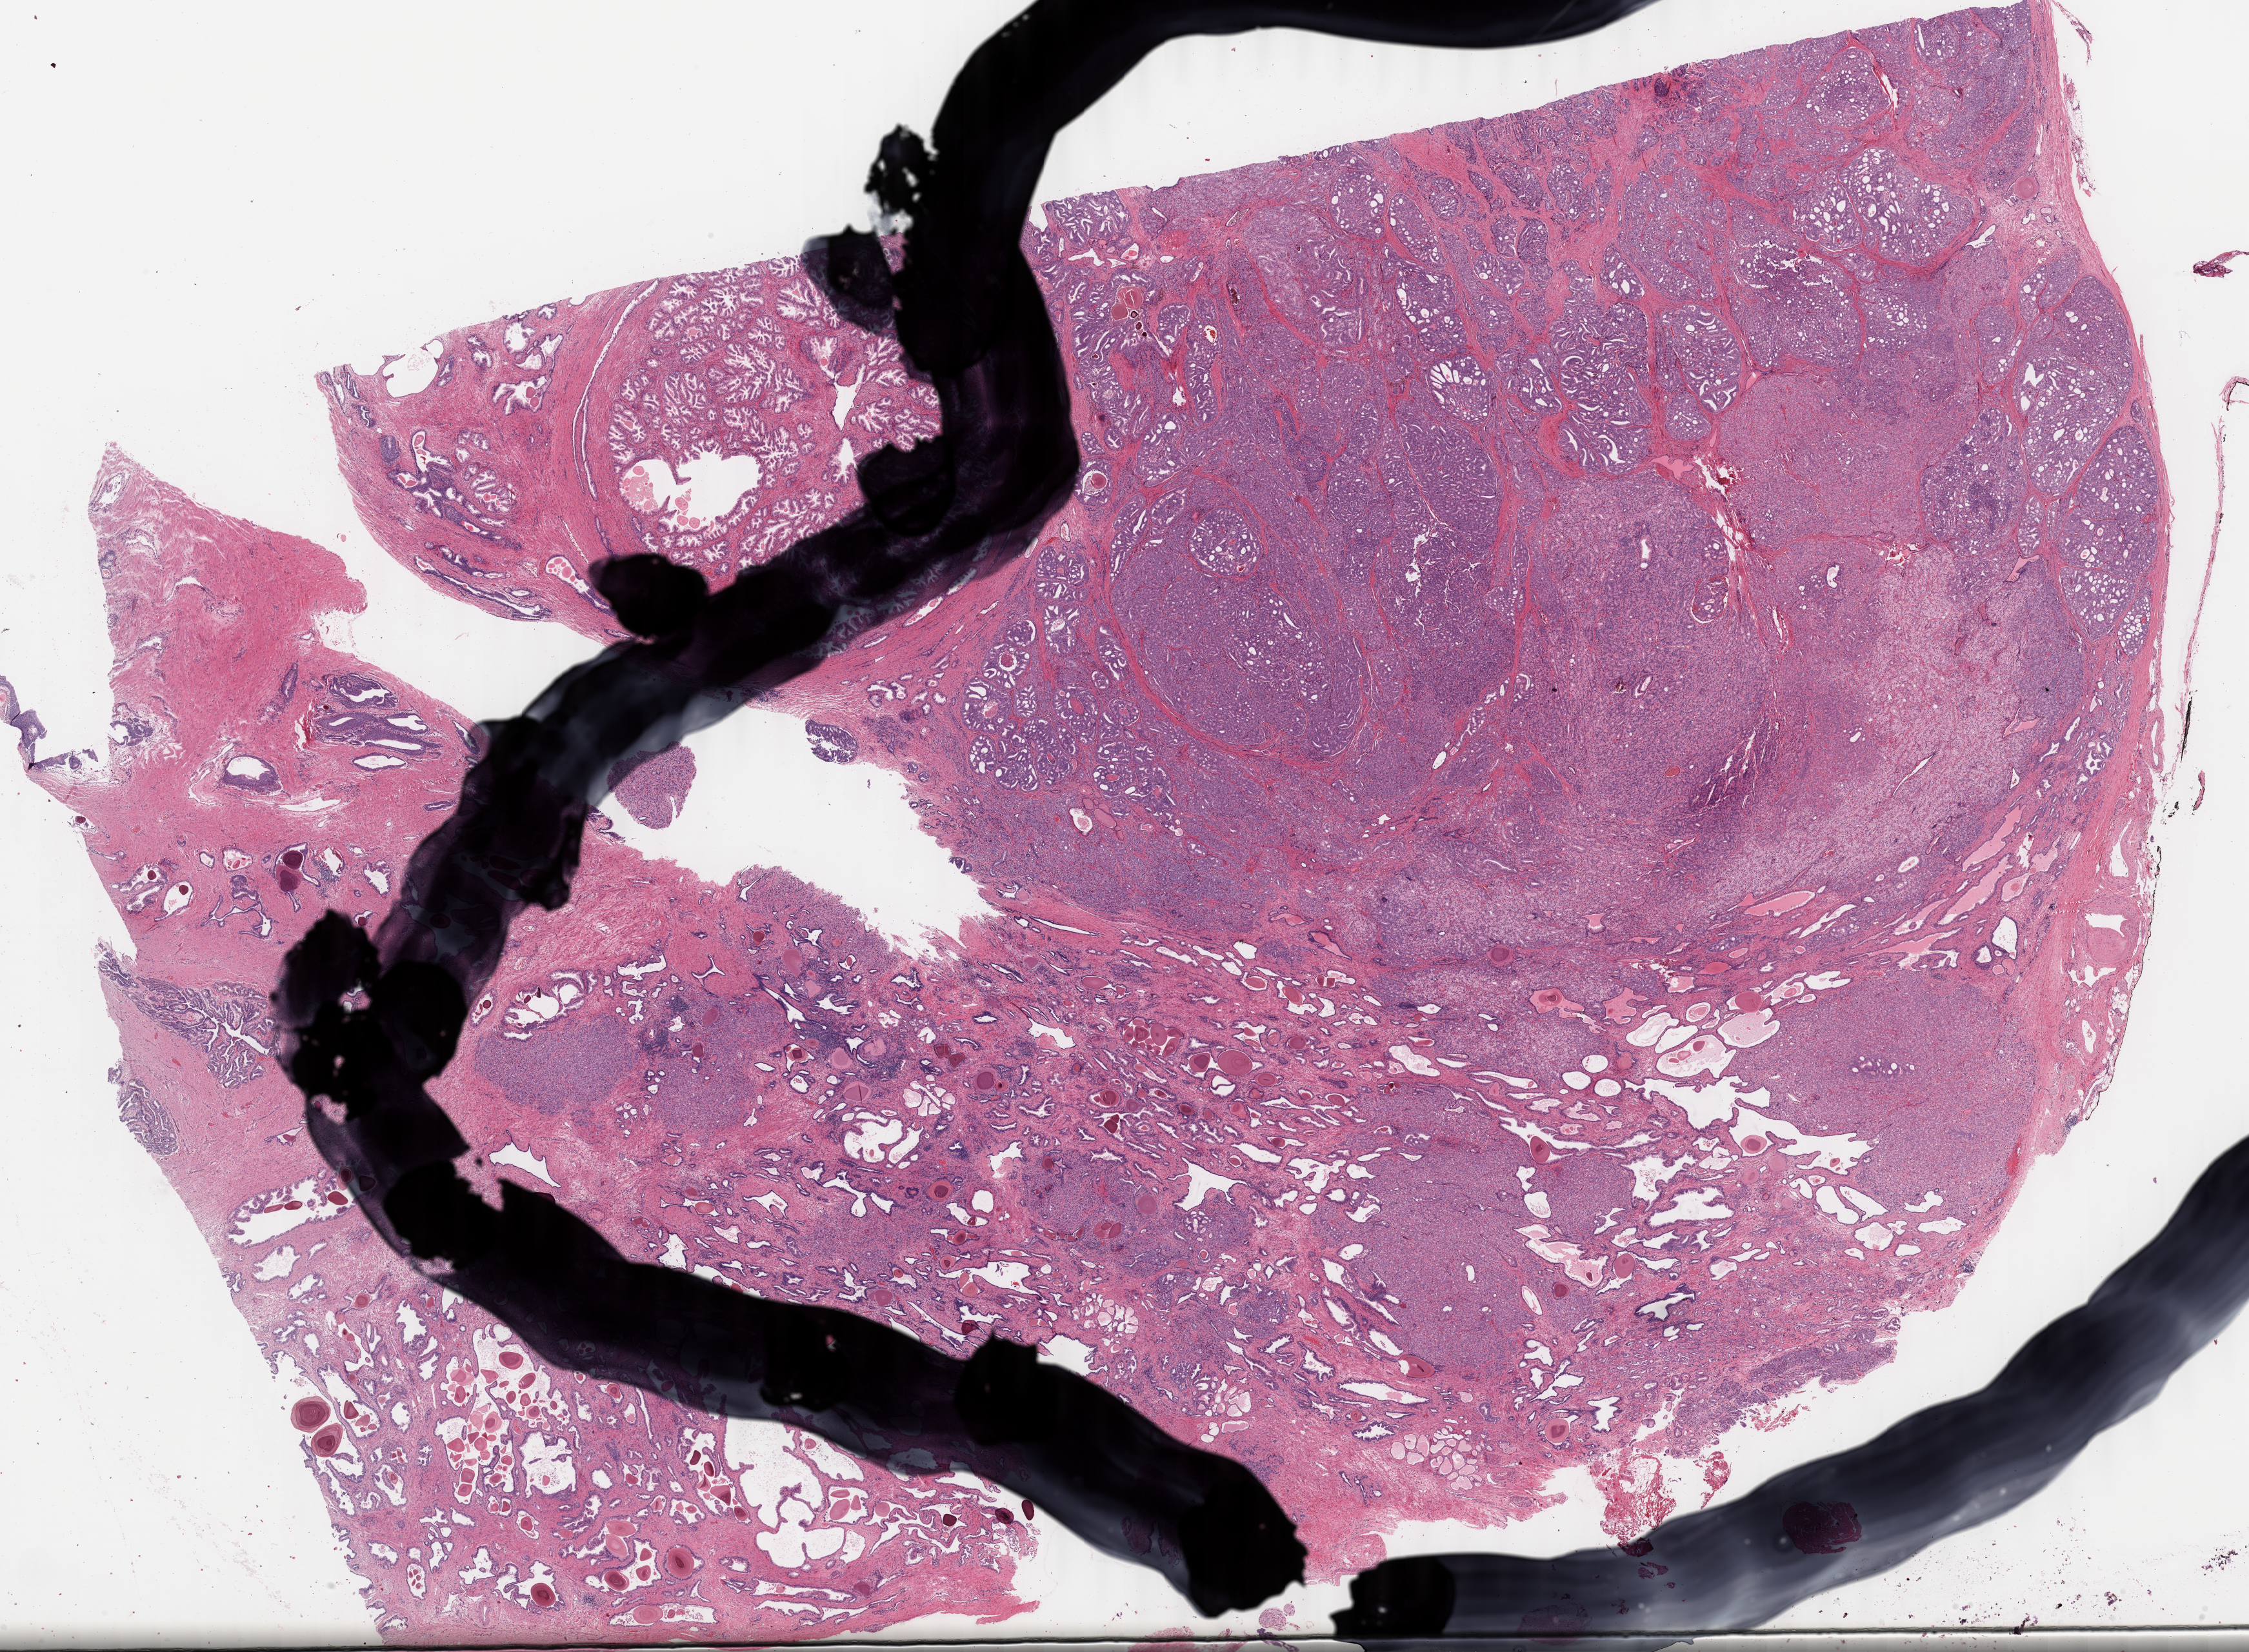
Whole-slide histology image, Hematoxylin and eosin (H&E) stained — whole scanned area (about 27.7 x 20.4 mm, slide scanned at 40x) shown as a low-resolution overview; FFPE section; sample: primary tumour, prostate. Male, age 68 years at initial diagnosis. Gleason score: 9 (4+5).
Lymph nodes positive (case pathology): 0 of 10 examined. Histologic diagnosis: Adenocarcinoma, NOS (prostate gland). Laterality: bilateral.